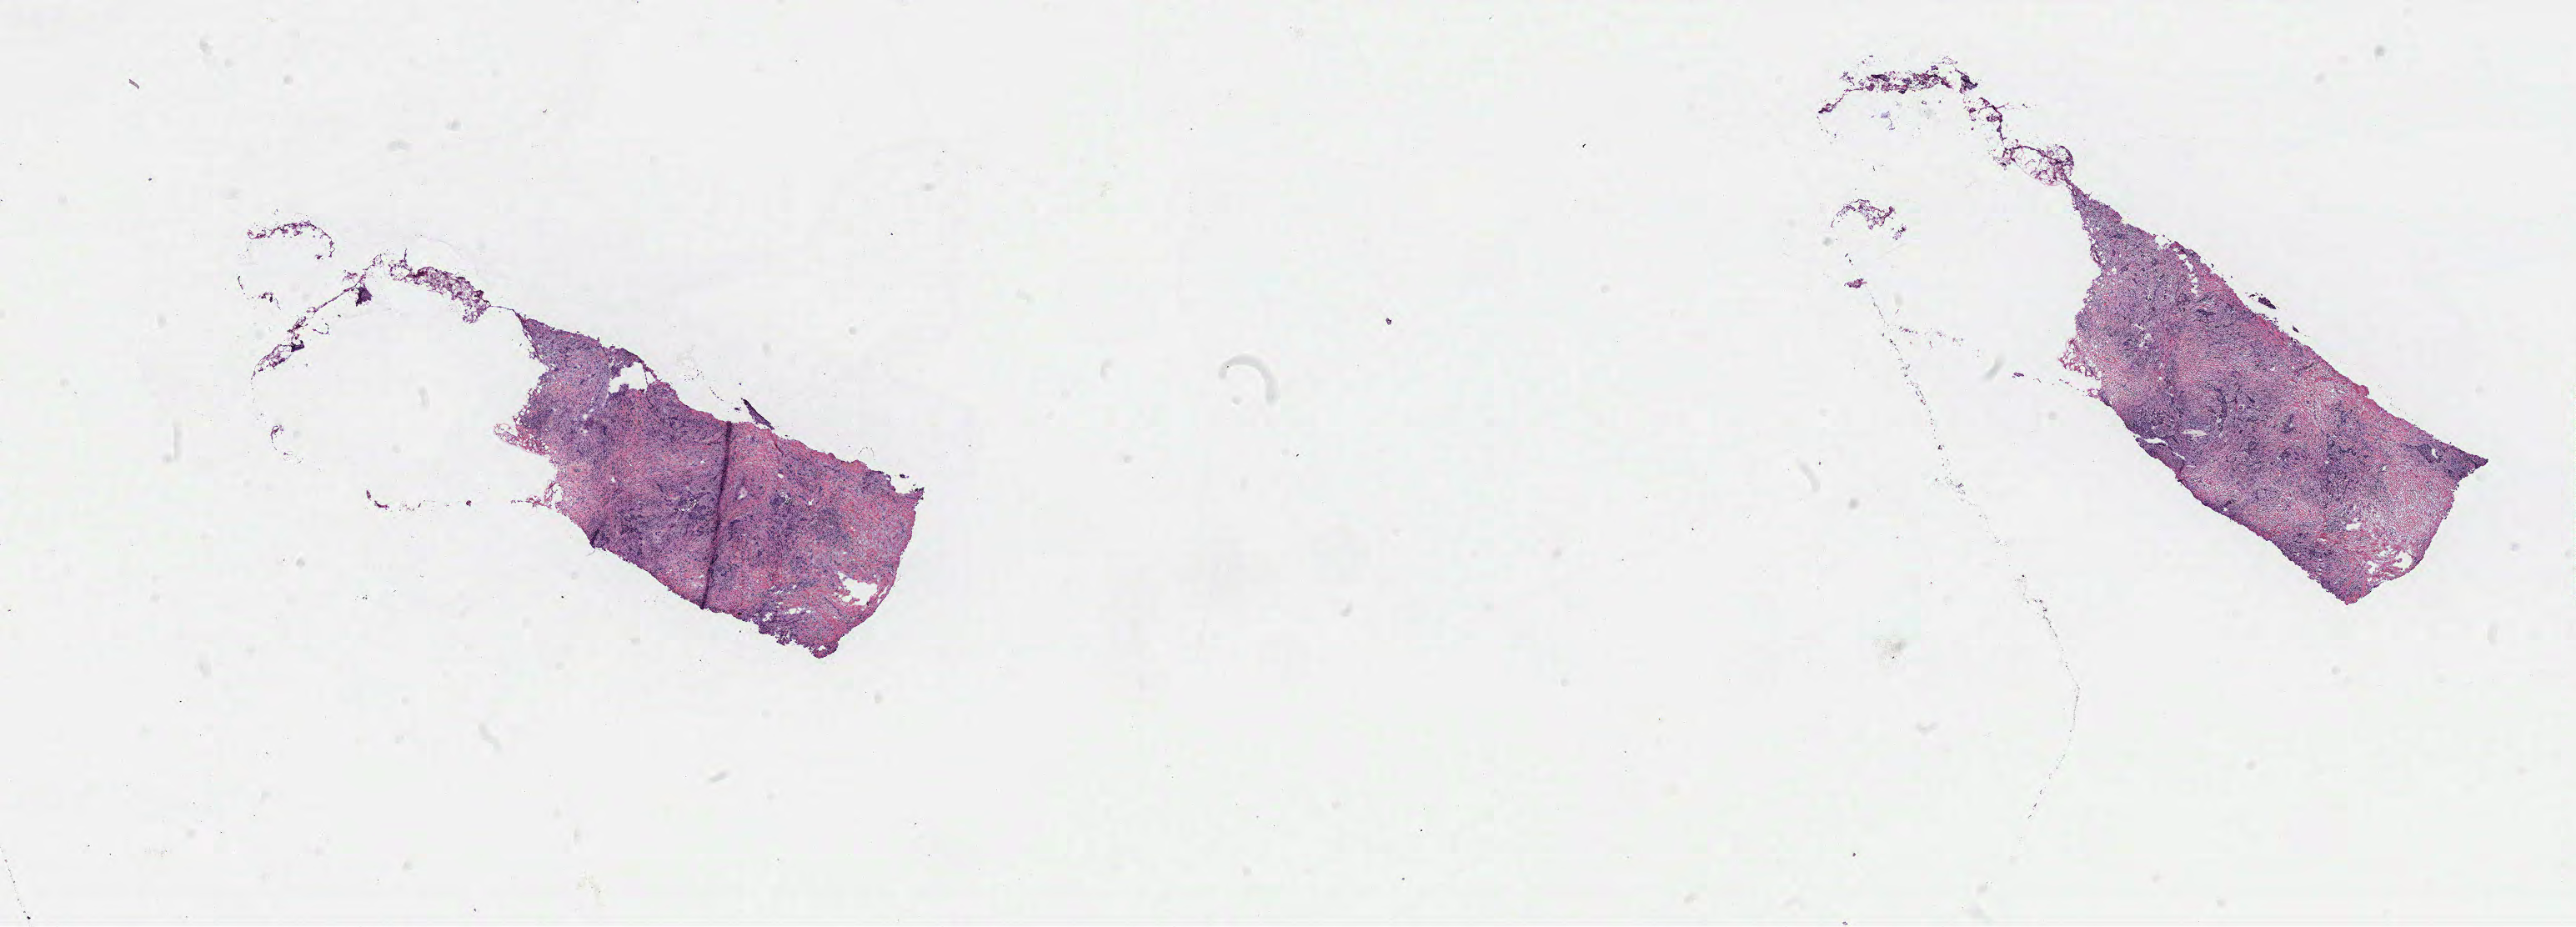
Digitized Hematoxylin and eosin (H&E) stained tissue section (whole slide) — a low-resolution overview of the entire scanned area, about 24.7 x 8.9 mm. Breast, tissue type not recorded.
* patient diagnosis (cohort enrolment): breast cancer (breast)